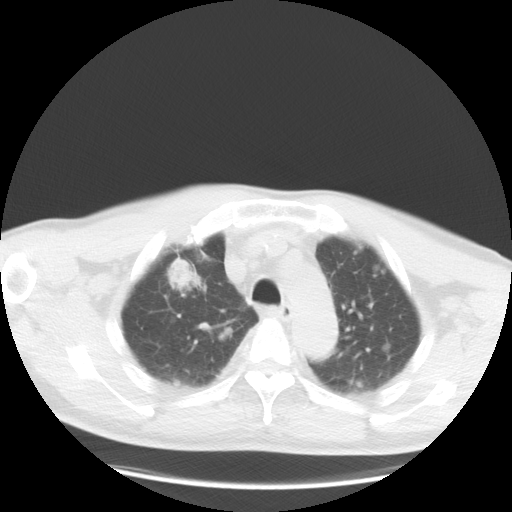
Chest CT, one axial slice; position 23 of 35 along the scan axis; reconstruction kernel STANDARD; 120 kVp; lung window (W 1500 / L -600 HU); 5 mm slice thickness; 512 × 512 image matrix, field of view 369 × 369 mm. Patient: male, 57 years. From the clinical record (not read from this slice): clinical TNM (as recorded): T2 N3 M1a.
Annotated regions visible in this slice (rectangle marked by the reading radiologist):
- lung tumour (recorded histology: adenocarcinoma): bounding box <166,253,197,289> (left, top, right, bottom; pixels)